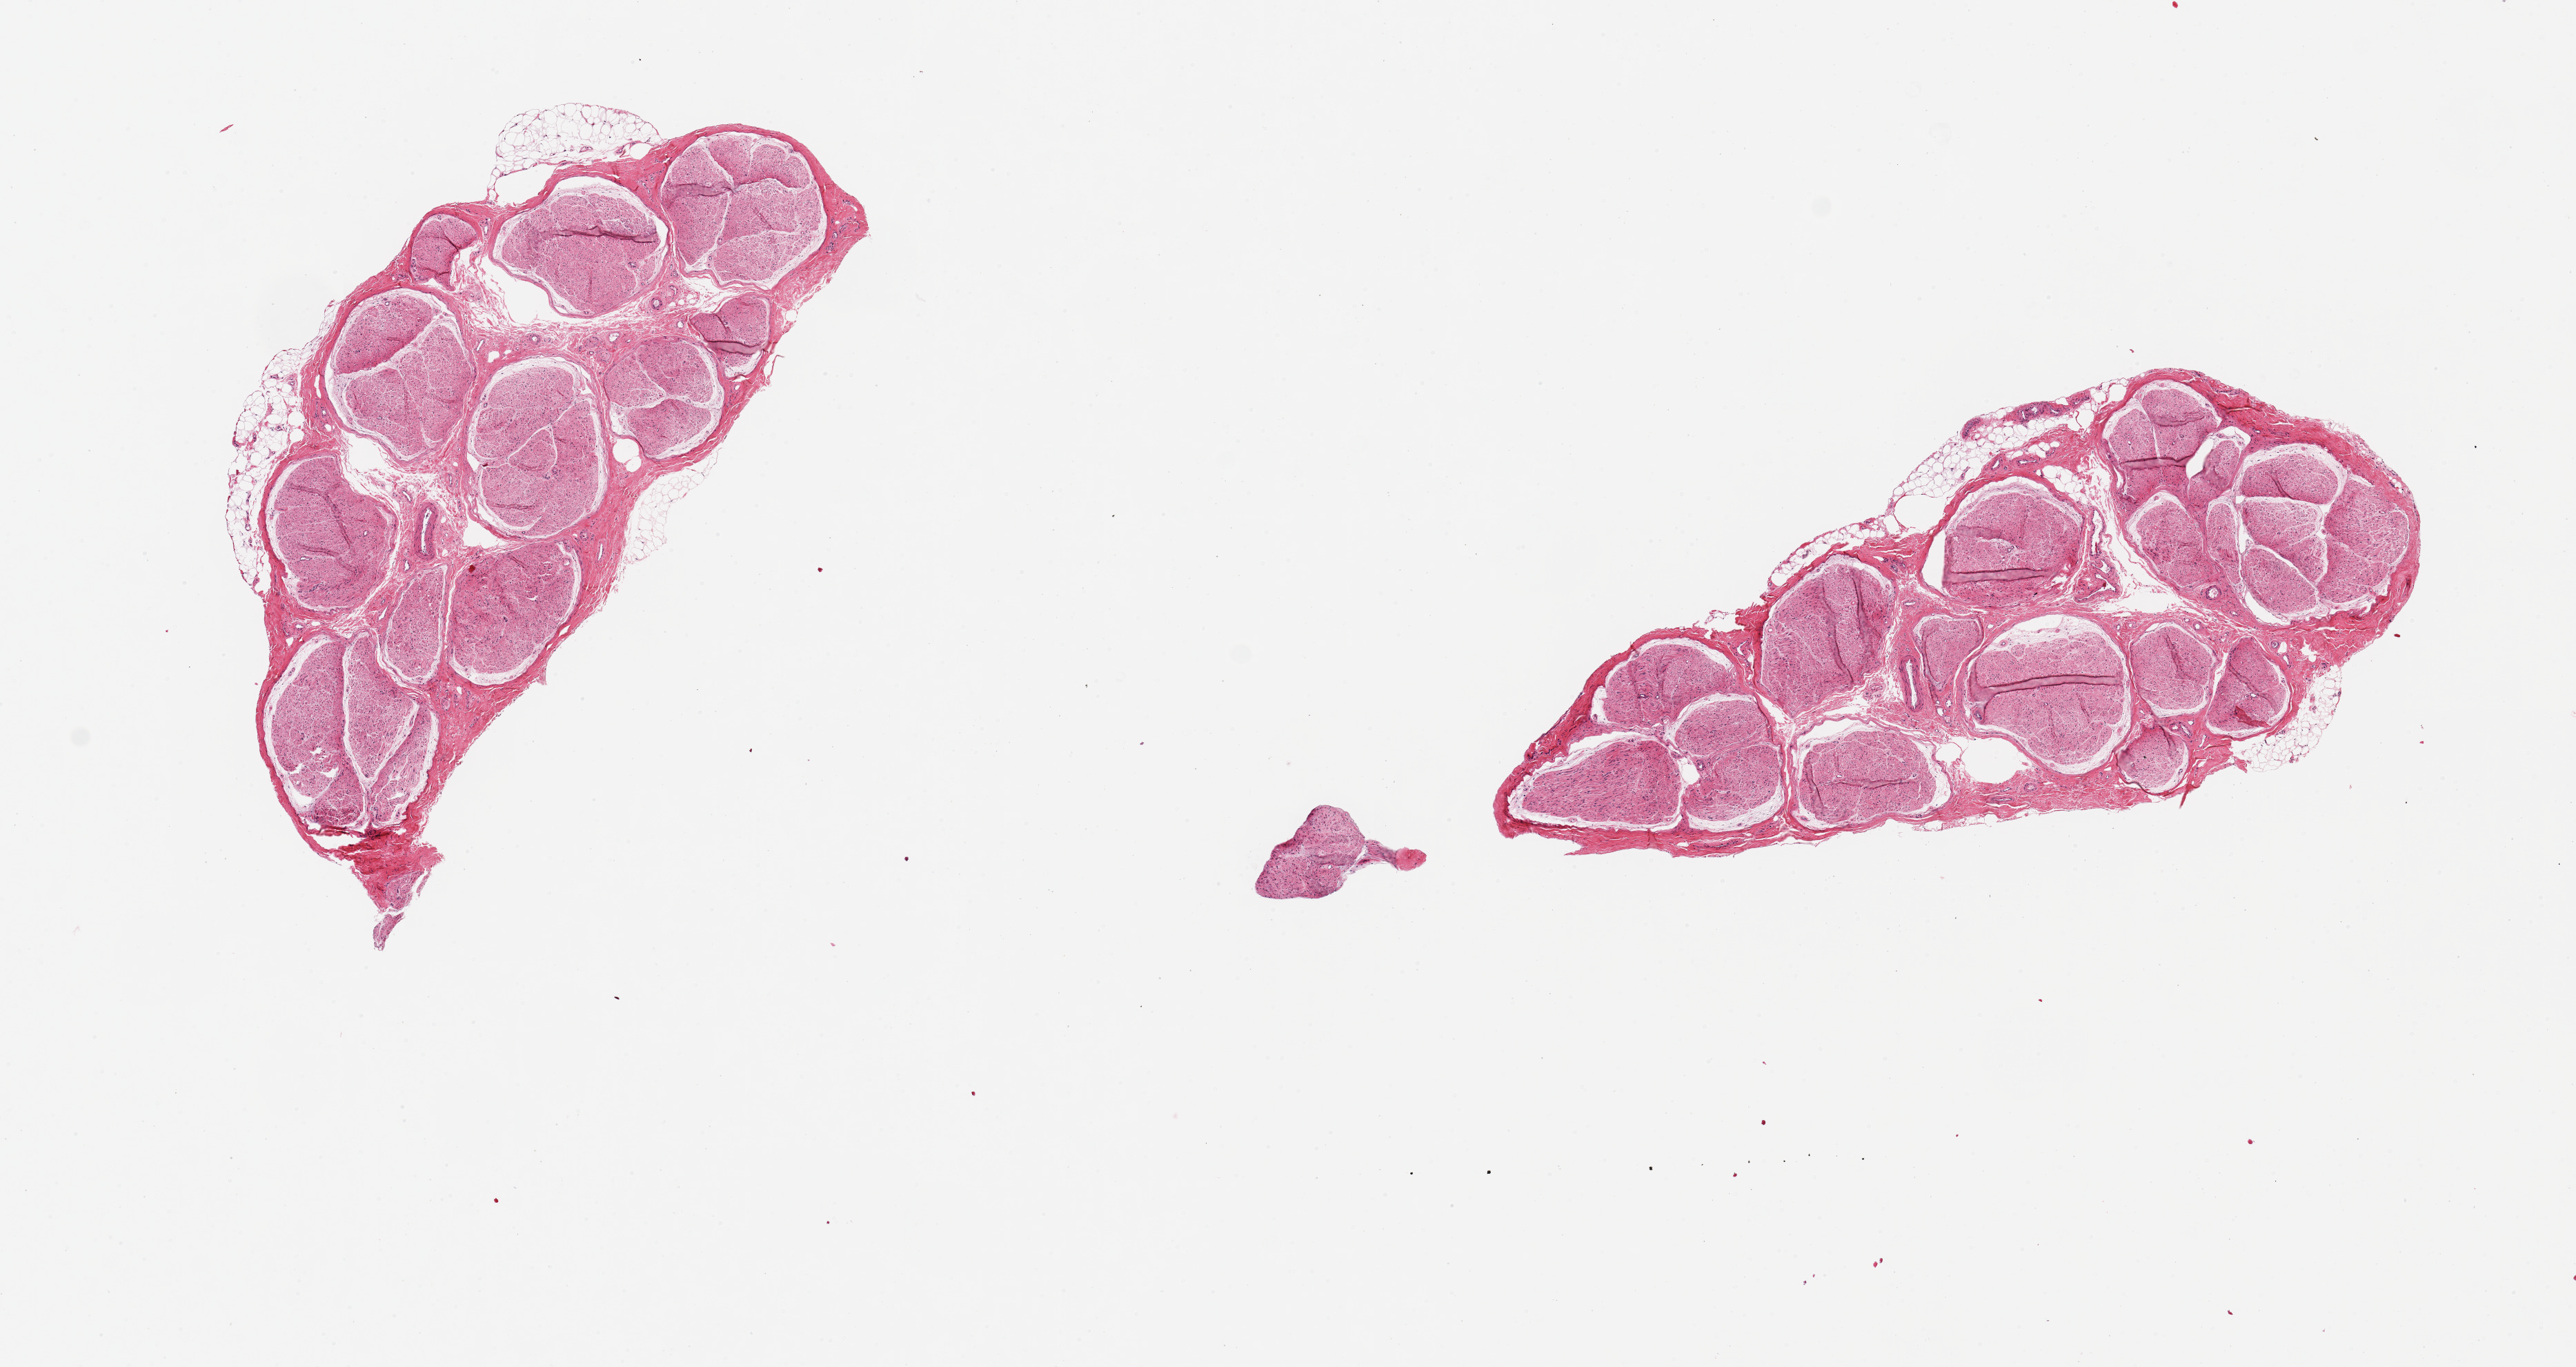
H&E whole-slide image, shown as a low-resolution overview of the whole scanned area (about 14.8 x 7.8 mm). PAXgene-fixed paraffin-embedded (PFPE) section. Sampled site (target tissue): tibial nerve. Donor tissue sample. Donor sex: male.
Pathologist's review note for this sample: 2 pieces, 5x2 & 7x2.5mm; Well trimmed nerve: <5% adipose.